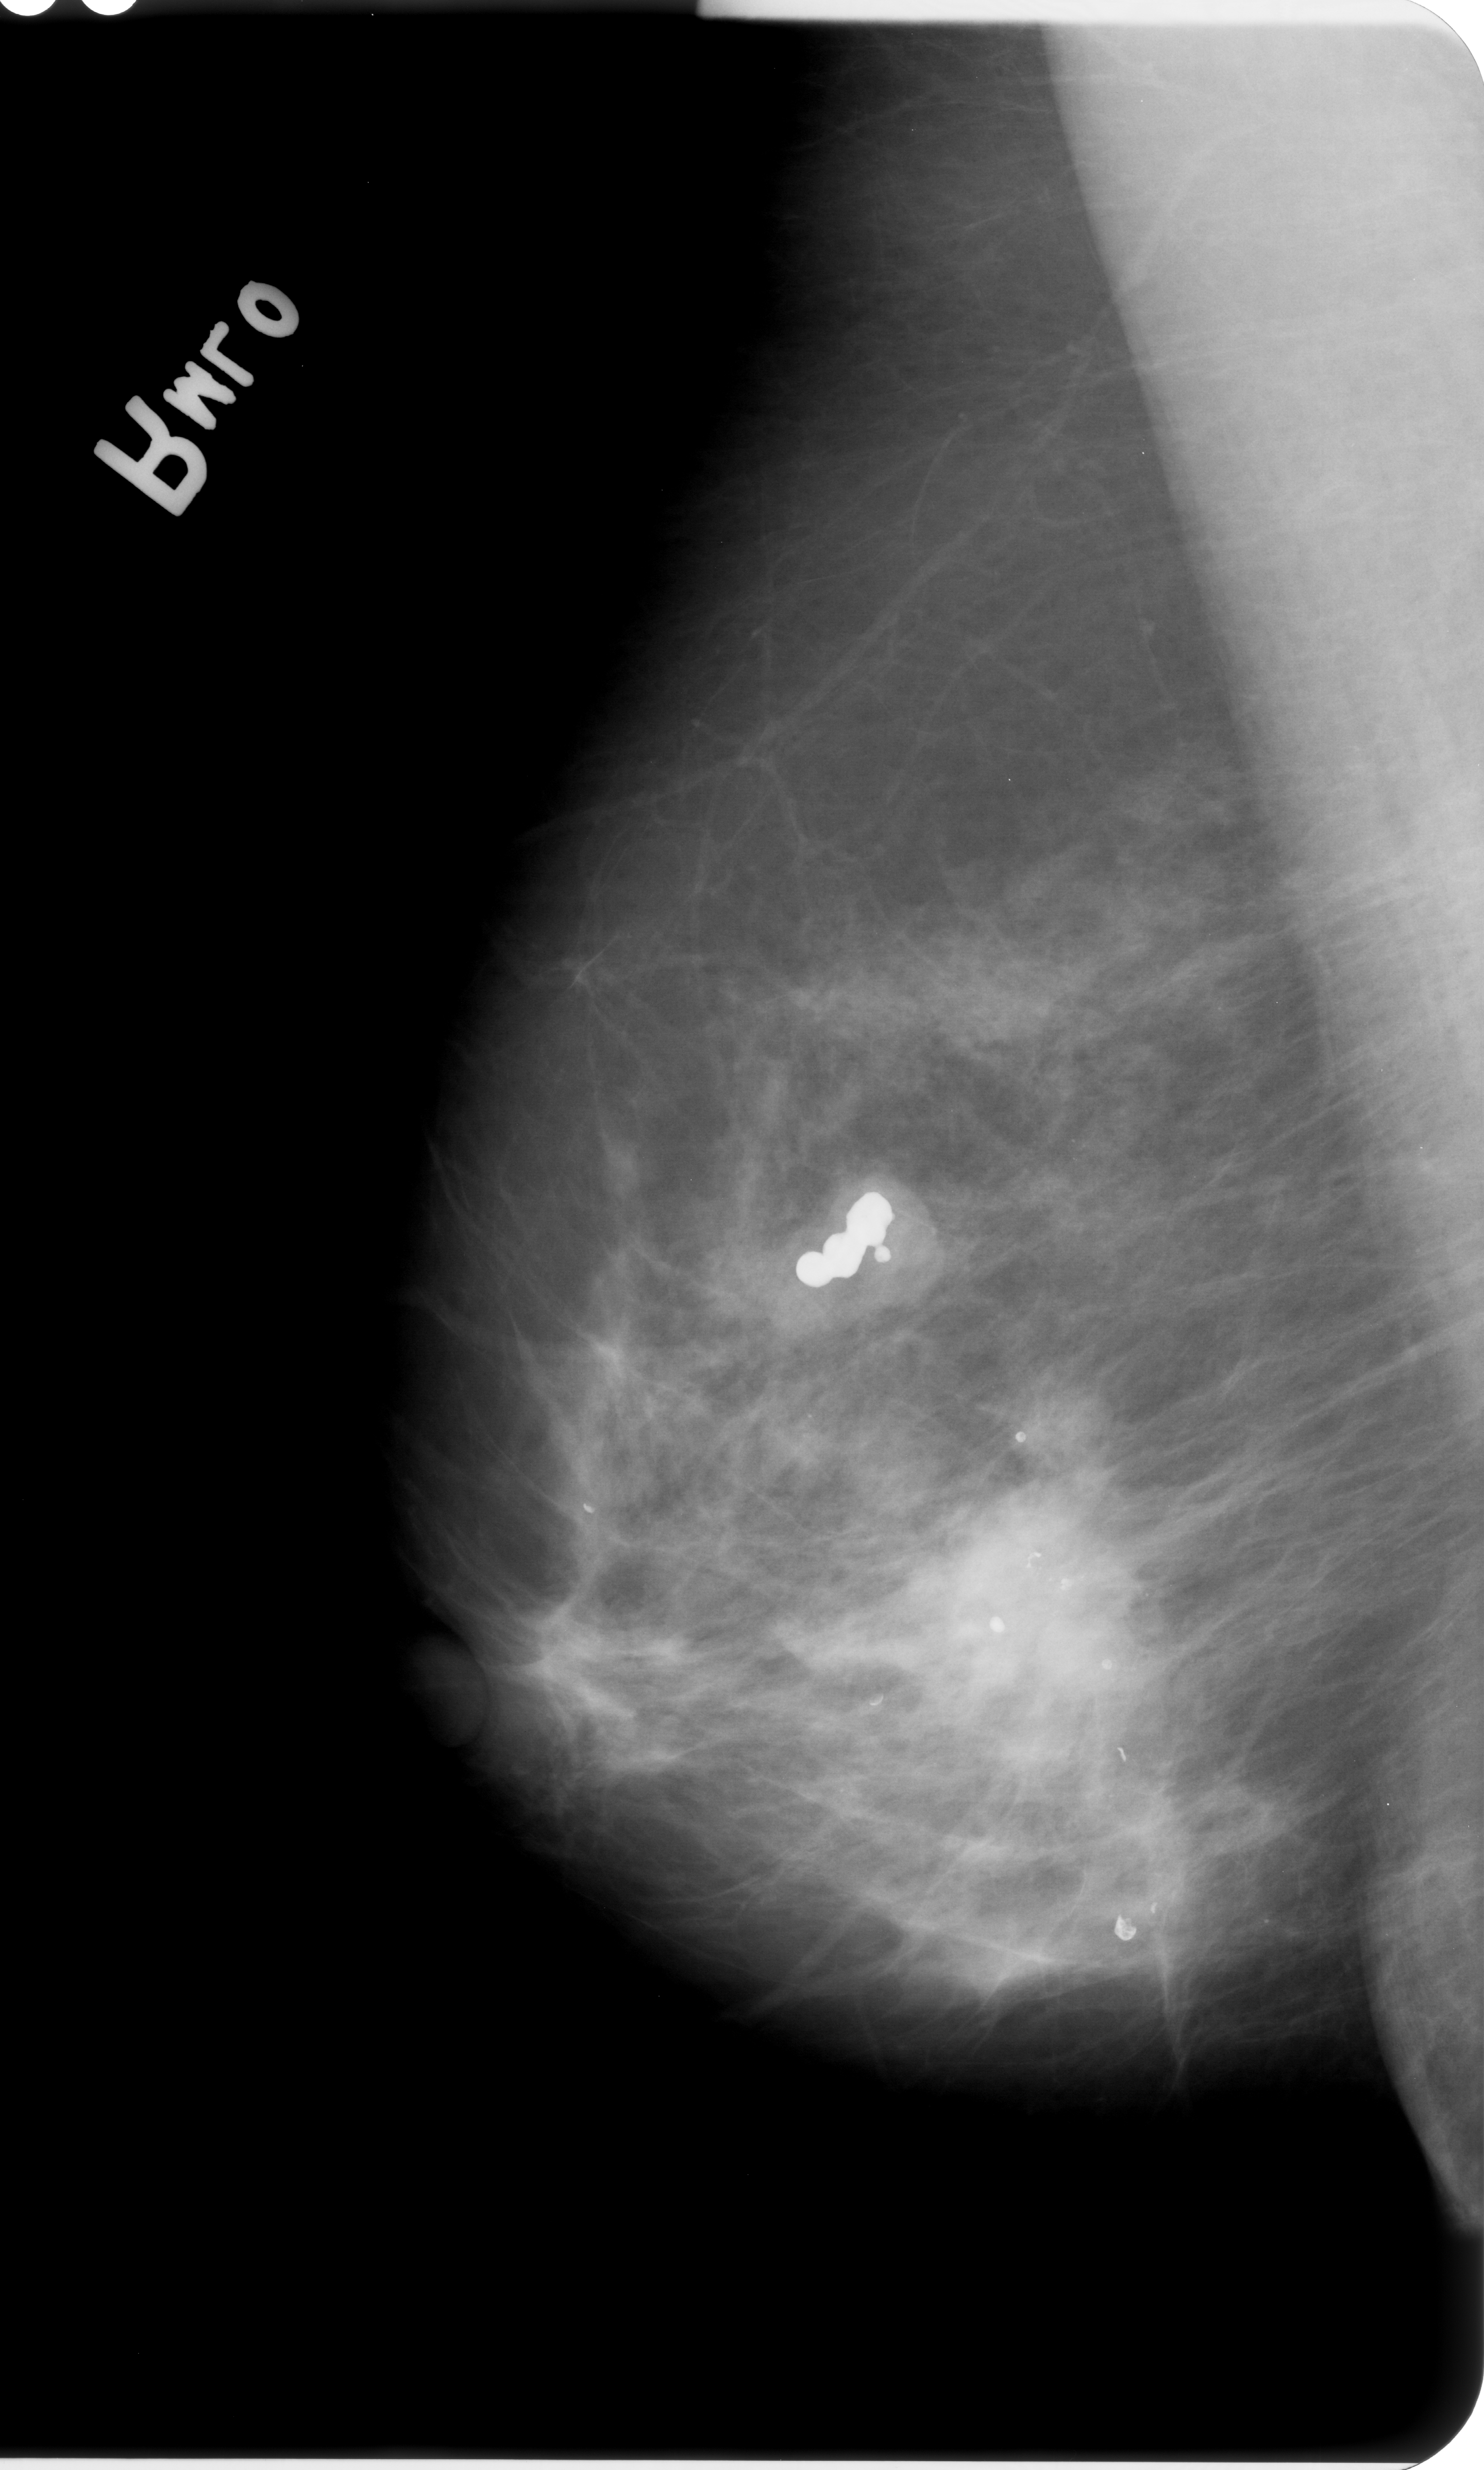
Mammogram (digitized film). Right breast. Mediolateral oblique (MLO) view. Breast composition: heterogeneously dense (BI-RADS density category 3 of 4). 1484 × 2470 image matrix.
Expert-marked regions of interest on this image (one box per marked abnormality):
- mass, shape architectural distortion, margins spiculated; BI-RADS assessment category 4; subtlety rating 4 on a 1 (subtle) to 5 (obvious) scale; pathology (as recorded): malignant: bounding box [x1, y1, x2, y2] px = [898, 1525, 1133, 1715]